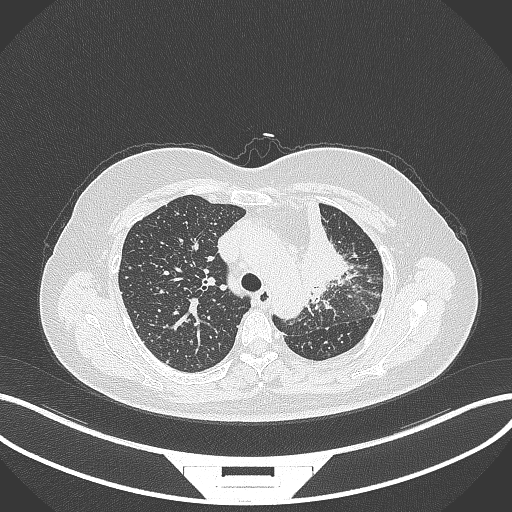
Chest CT, one axial slice. Slice 242 of 348 in the series (ordered by position). Reconstruction kernel B70f. 120 kVp. Lung window (W 1500 / L -600 HU). 512 × 512 image matrix, field of view 400 × 400 mm. Female patient, age 49 years. Case-level facts recorded for this patient, not image findings: clinical TNM (as recorded): T1c N0 M1.
Outlined on this slice (bounding box drawn by a radiologist):
- lung tumour (recorded histology: adenocarcinoma): box from (x=301, y=203) to (x=347, y=301) px